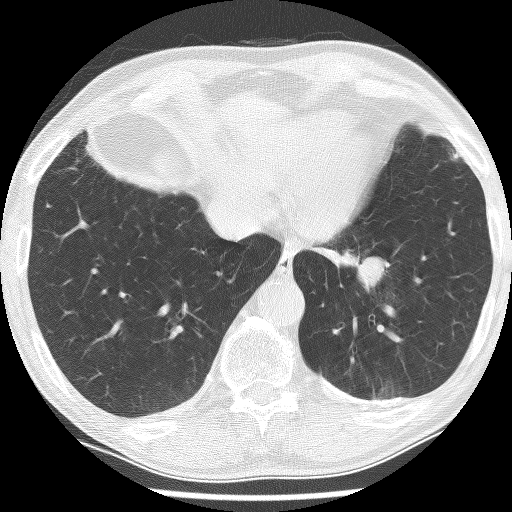
Low-dose screening chest CT, axial slice, baseline screening round, lung window (W 1500 / L -600 HU), 2.5 mm slice thickness, lung (sharp) reconstruction kernel (BONE), slice 186 of 226 in the series, 512 × 512 image matrix. Male, age 74 years at enrolment. Current smoker at enrolment.
Expert-annotated lung lesion, bounding box <312,214,411,306> (left, top, right, bottom; pixels). Reader record for this screening exam (exam-level; its link to the box is not recorded): non-calcified nodule or mass ≥4 mm, left lower lobe, 30 × 27 mm, spiculated (stellate) margins, soft tissue attenuation. Official screen result: positive, change unspecified: nodule(s) >= 4 mm or enlarging nodule(s), mass(es), or other non-specific abnormalities suspicious for lung cancer. Participant outcome: lung cancer diagnosed 151 days after this screen — adenocarcinoma, NOS, left lower lobe, stage IIIA (AJCC 6th edition), 49 mm at pathology.